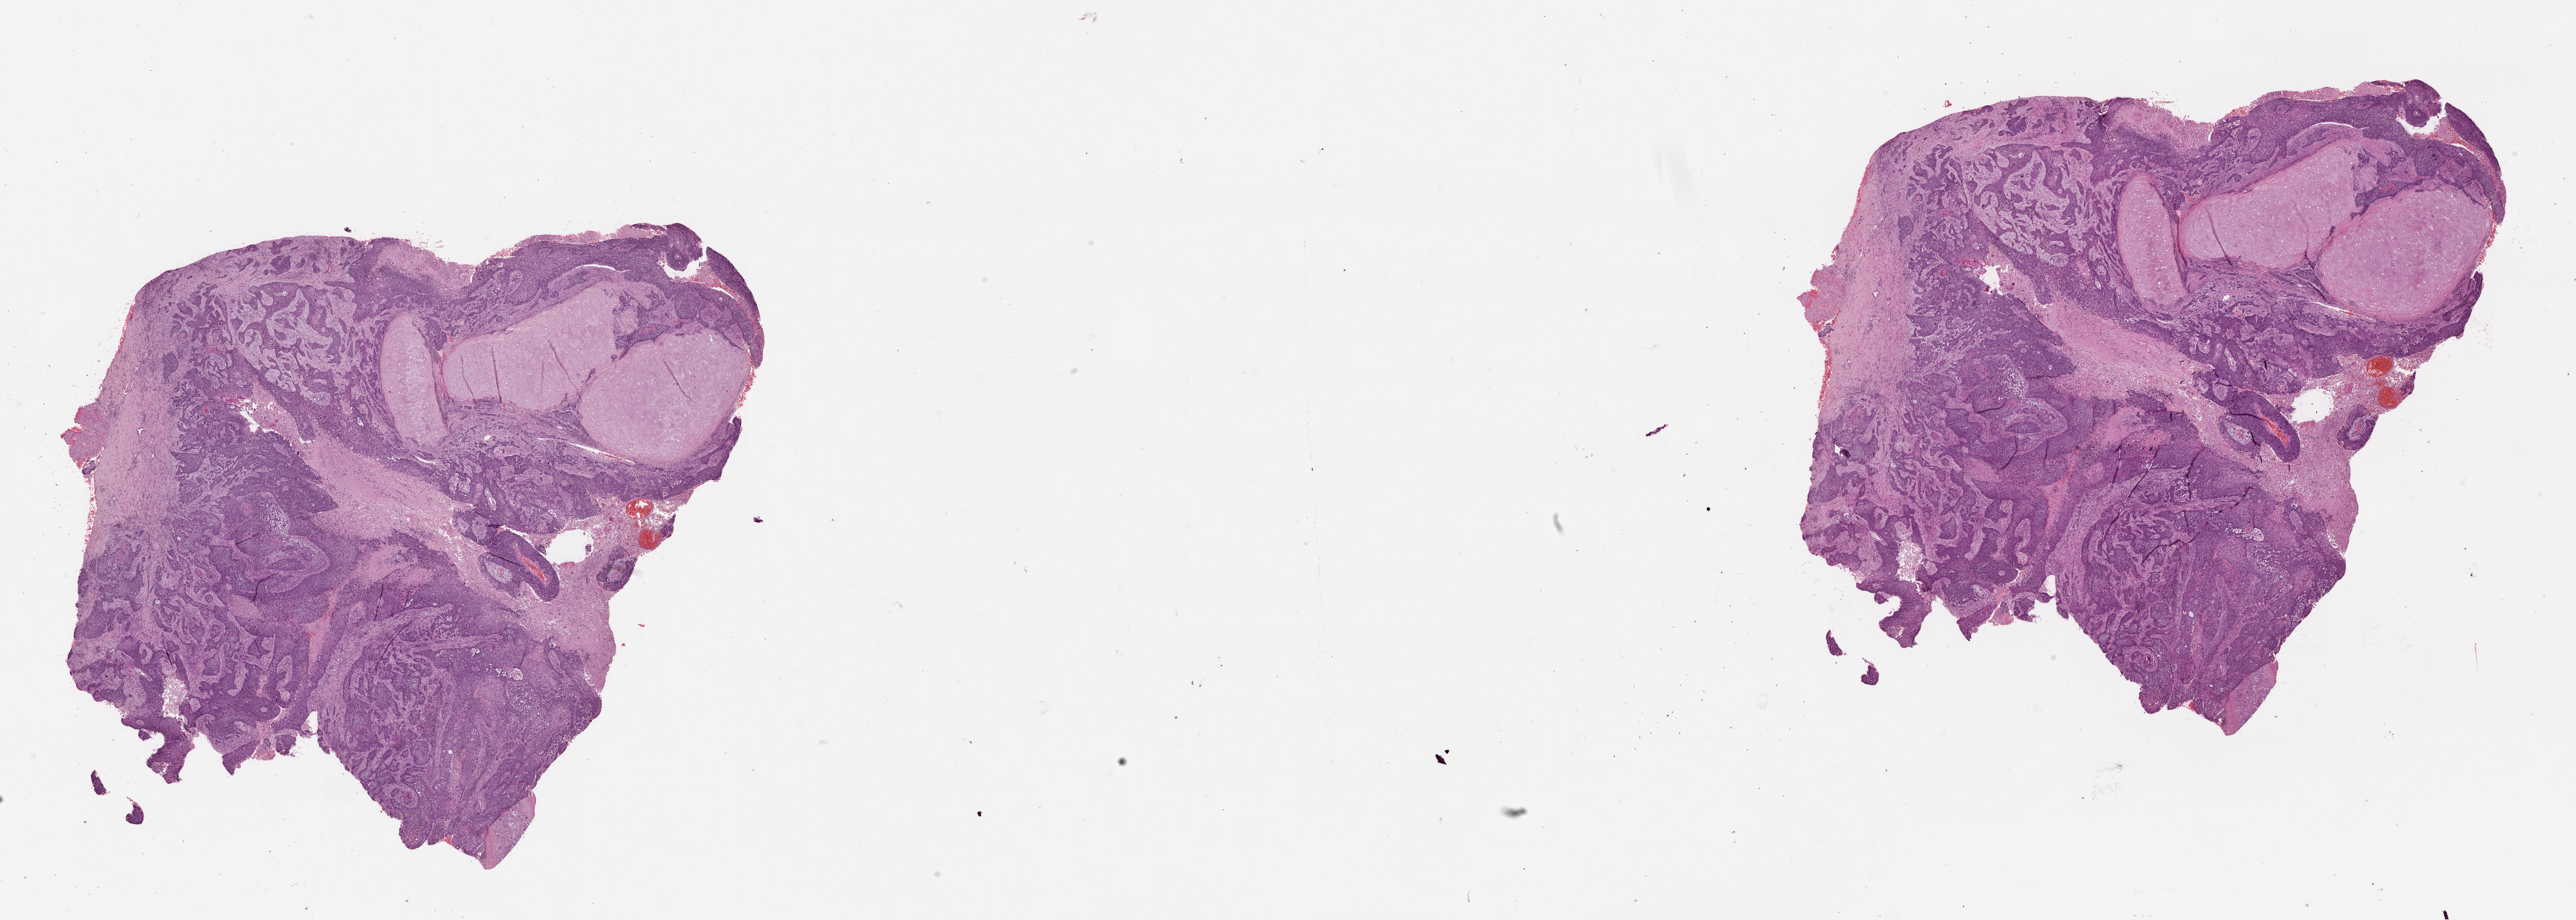
Digitized H&E-stained tissue section (whole slide) — shown as a low-resolution overview of the whole scanned area (about 31.1 x 11.1 mm, slide scanned at 20x), tumour tissue sample, lung. 59-year-old male patient.
Patient diagnosis (cohort enrolment): squamous cell carcinoma (lung).